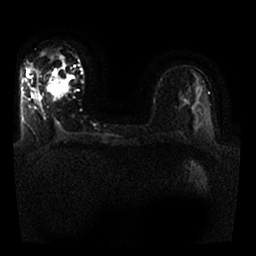
Breast MRI, one axial slice; diffusion-weighted series; image 2 of 4 stored at this slice position (different b-values; order by instance number); 1.5 T; 4 mm slice thickness; 256 × 256 image matrix. Female patient.
Structures marked on this image (expert manual segmentation):
- tumour on diffusion-weighted imaging: bounding box (x1, y1, x2, y2) in pixels: (52, 75, 62, 84)